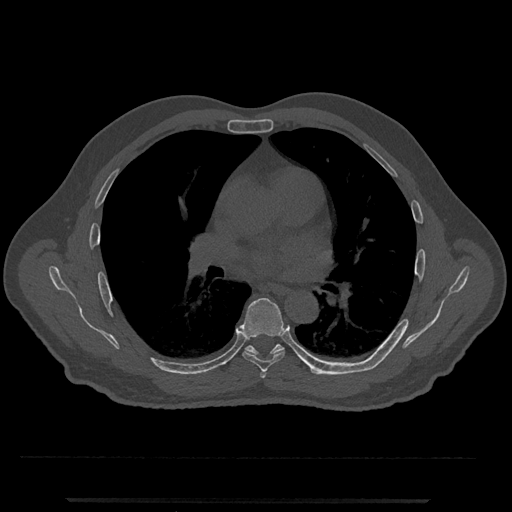
CT including the spine, one axial slice. Position 721 of 797 along the scan axis. 120 kVp. Bone window (W 1800 / L 400 HU). 0.5 mm slice thickness. 512 × 512 image matrix, field of view 419 × 419 mm. Male patient, age 63 years. From the clinical record (not read from this slice): primary cancer: prostate.
Structures marked on this image (semi-automatic segmentation, software-assisted and operator-edited):
- T5 vertebra: bounding box <260,371,267,379> (left, top, right, bottom; pixels)
- T6 vertebra: <240,298,285,372>
- T7 vertebra: <245,344,329,375>